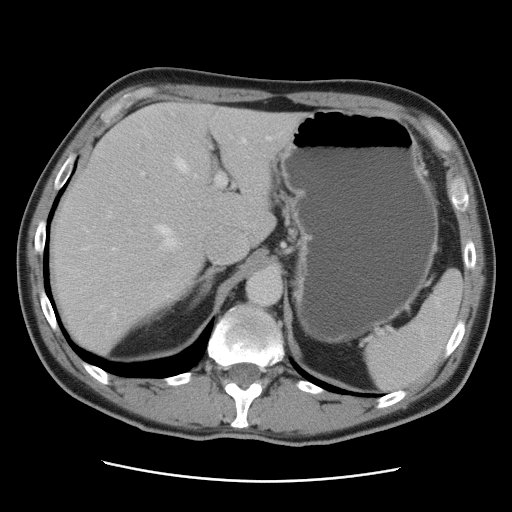
Contrast-enhanced abdominal CT, one axial slice; slice 62 of 89 in the series (ordered by position); 120 kVp; intravenous contrast given; soft-tissue window (W 400 / L 40 HU); 512 × 512 image matrix. Male patient, age 59 years. Case-level facts recorded for this patient, not image findings: diagnosis: colorectal cancer liver metastases, imaged before liver resection; multiple liver metastases: yes; largest metastasis: 0.6 cm.
Outlined on this slice (outlined manually by an expert reader):
- hepatic veins: bounding box <72,137,271,295> (left, top, right, bottom; pixels)
- liver: <51,103,307,354>
- planned liver remnant (the part of the liver to remain after resection): <91,103,284,245>
- portal vein (with intrahepatic branches): <130,172,226,232>